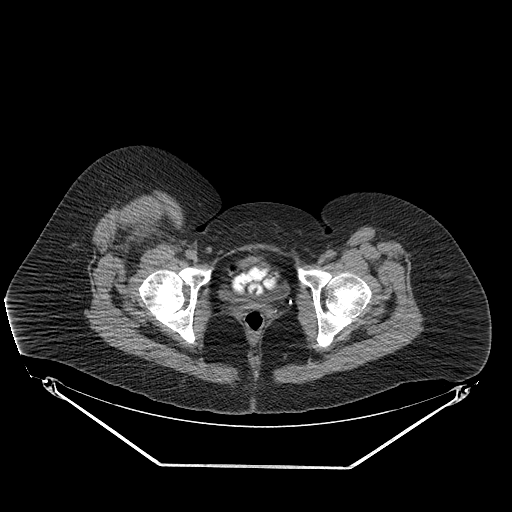
CT of an extremity soft-tissue mass (from a PET/CT study), one axial slice; slice 67 of 267 in the series (ordered by position); reconstruction kernel STANDARD; soft-tissue window (W 400 / L 40 HU); 512 × 512 image matrix, field of view 500 × 500 mm. Female patient. From the clinical record (not read from this slice): histological type: malignant solitary fibrous tumor; grade: intermediate; site of the primary tumour: right thigh.
Annotated regions visible in this slice (expert contour drawn on MRI and transferred to this co-registered scan by the dataset authors):
- gross tumour volume including surrounding oedema: bounding box [x1, y1, x2, y2] px = [109, 210, 168, 243]